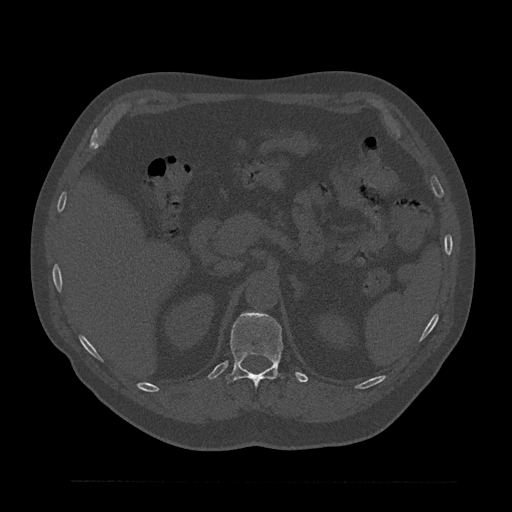
CT including the spine, one axial slice; position 227 of 797 along the scan axis; reconstruction kernel Br40s/3; bone window (W 1800 / L 400 HU); 0.5 mm slice thickness; 512 × 512 image matrix. Male patient, age 61 years. From the clinical record (not read from this slice): primary cancer: prostate.
Structures marked on this image (semi-automatically segmented with operator editing):
- T12 vertebra: bounding box [x1, y1, x2, y2] px = [227, 312, 285, 386]